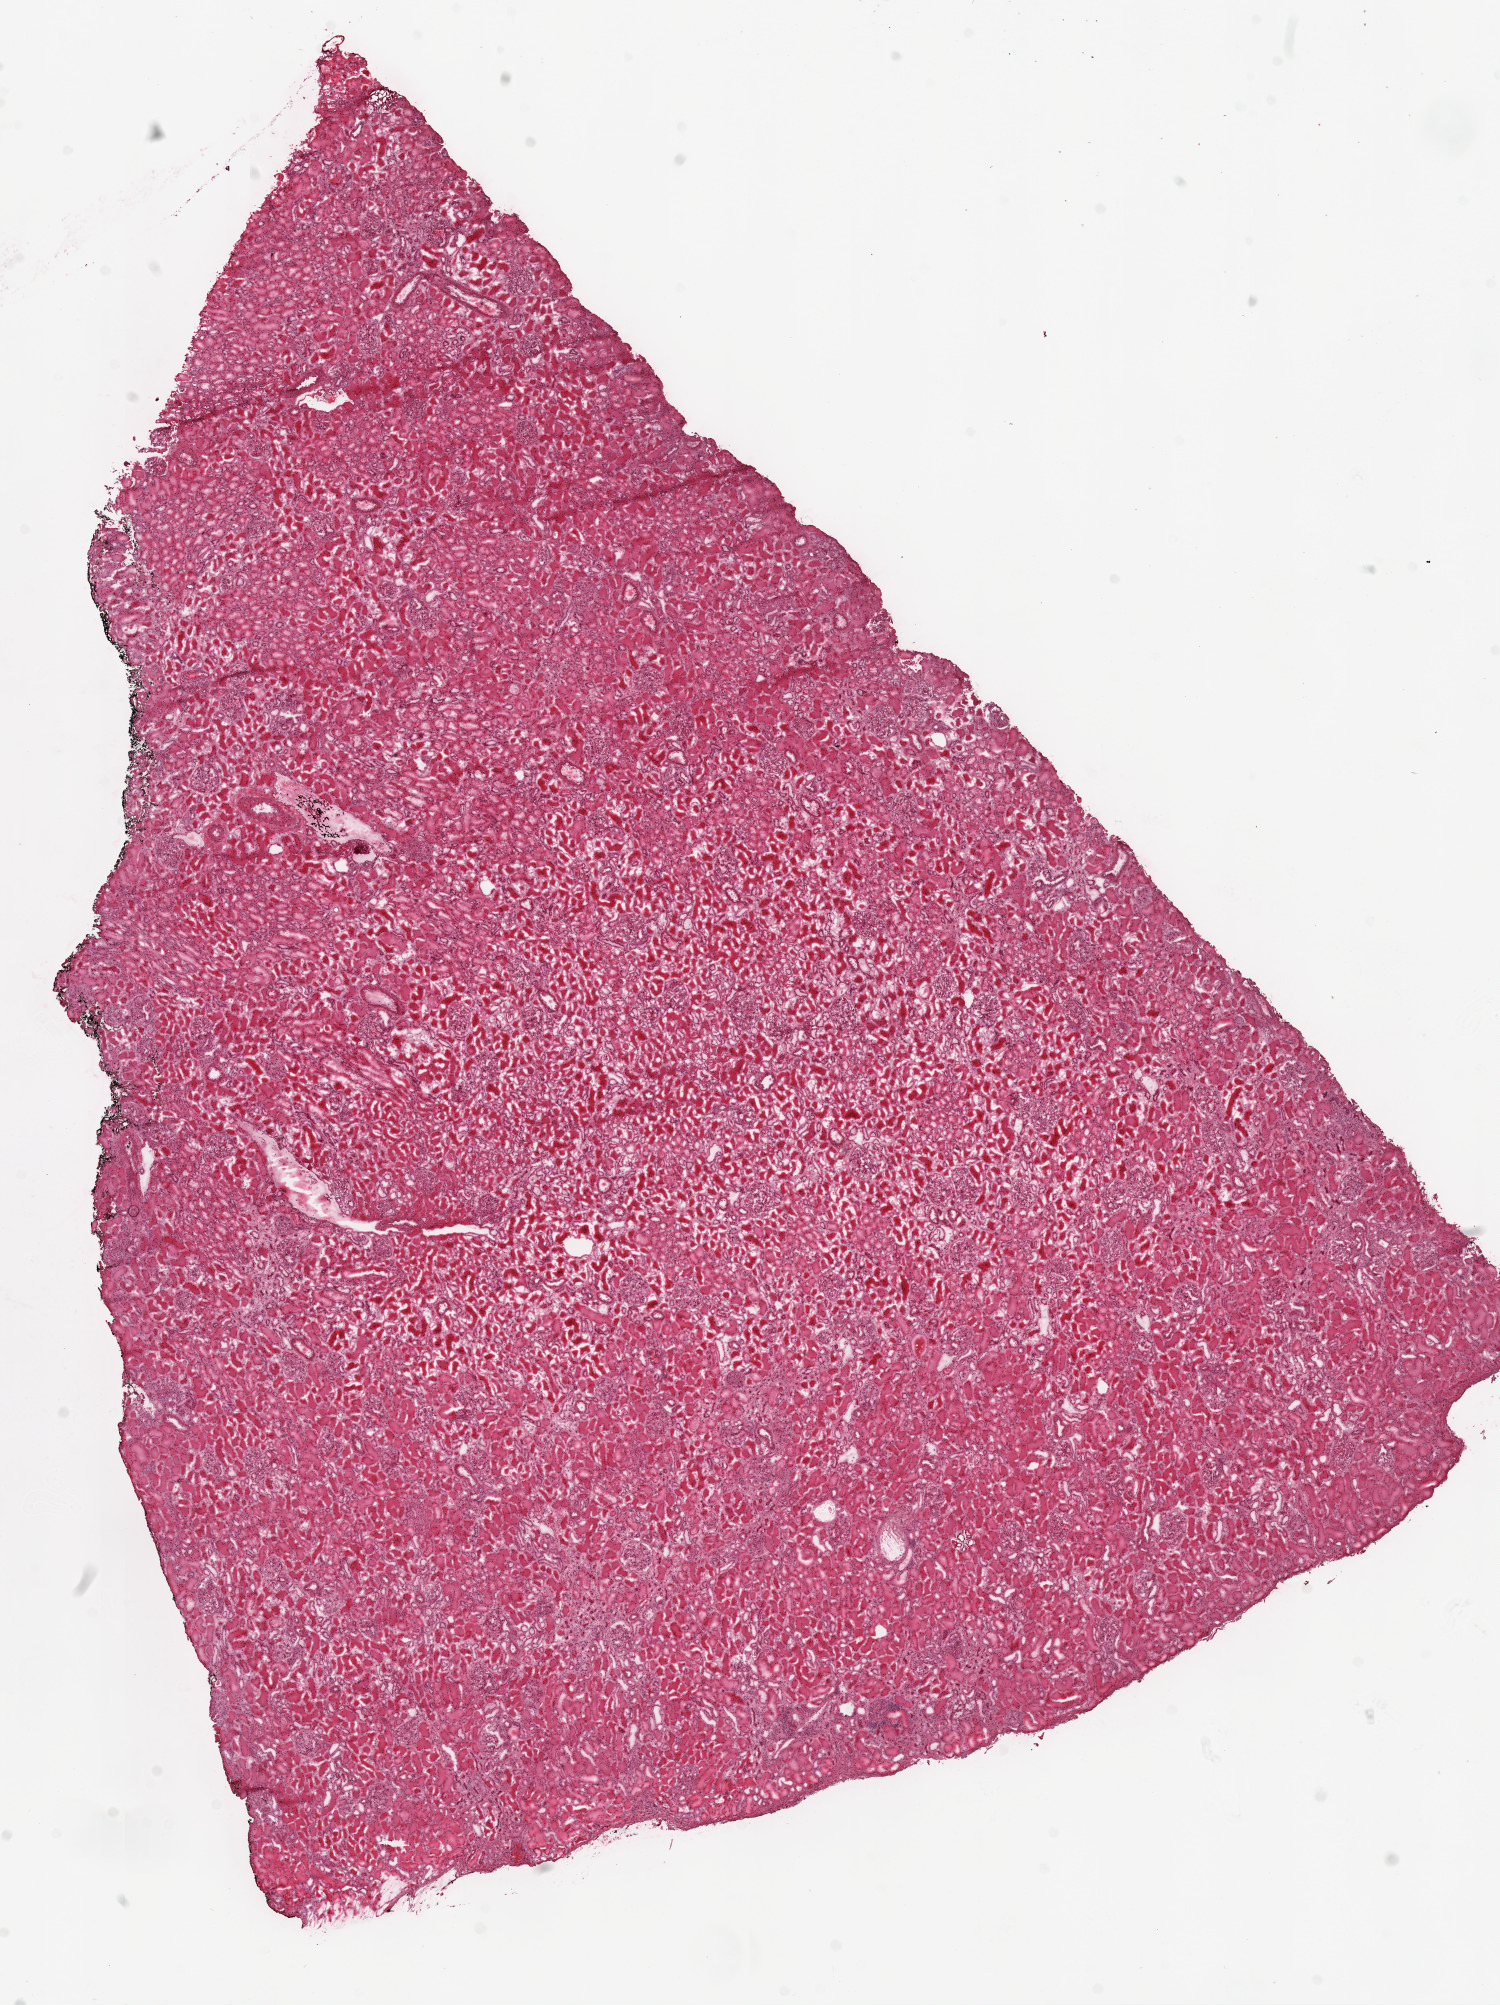
Whole-slide histology image, Hematoxylin and eosin (H&E) stained — low-resolution overview of the scanned area, about 12.0 x 16.1 mm. Frozen section from the top of the tissue portion. Sample: solid tissue normal (non-tumour tissue), kidney. Male patient; age at initial diagnosis 53 years.
This section: solid tissue normal (non-tumour) sample from the same patient. Patient diagnosis: Clear cell adenocarcinoma, NOS.